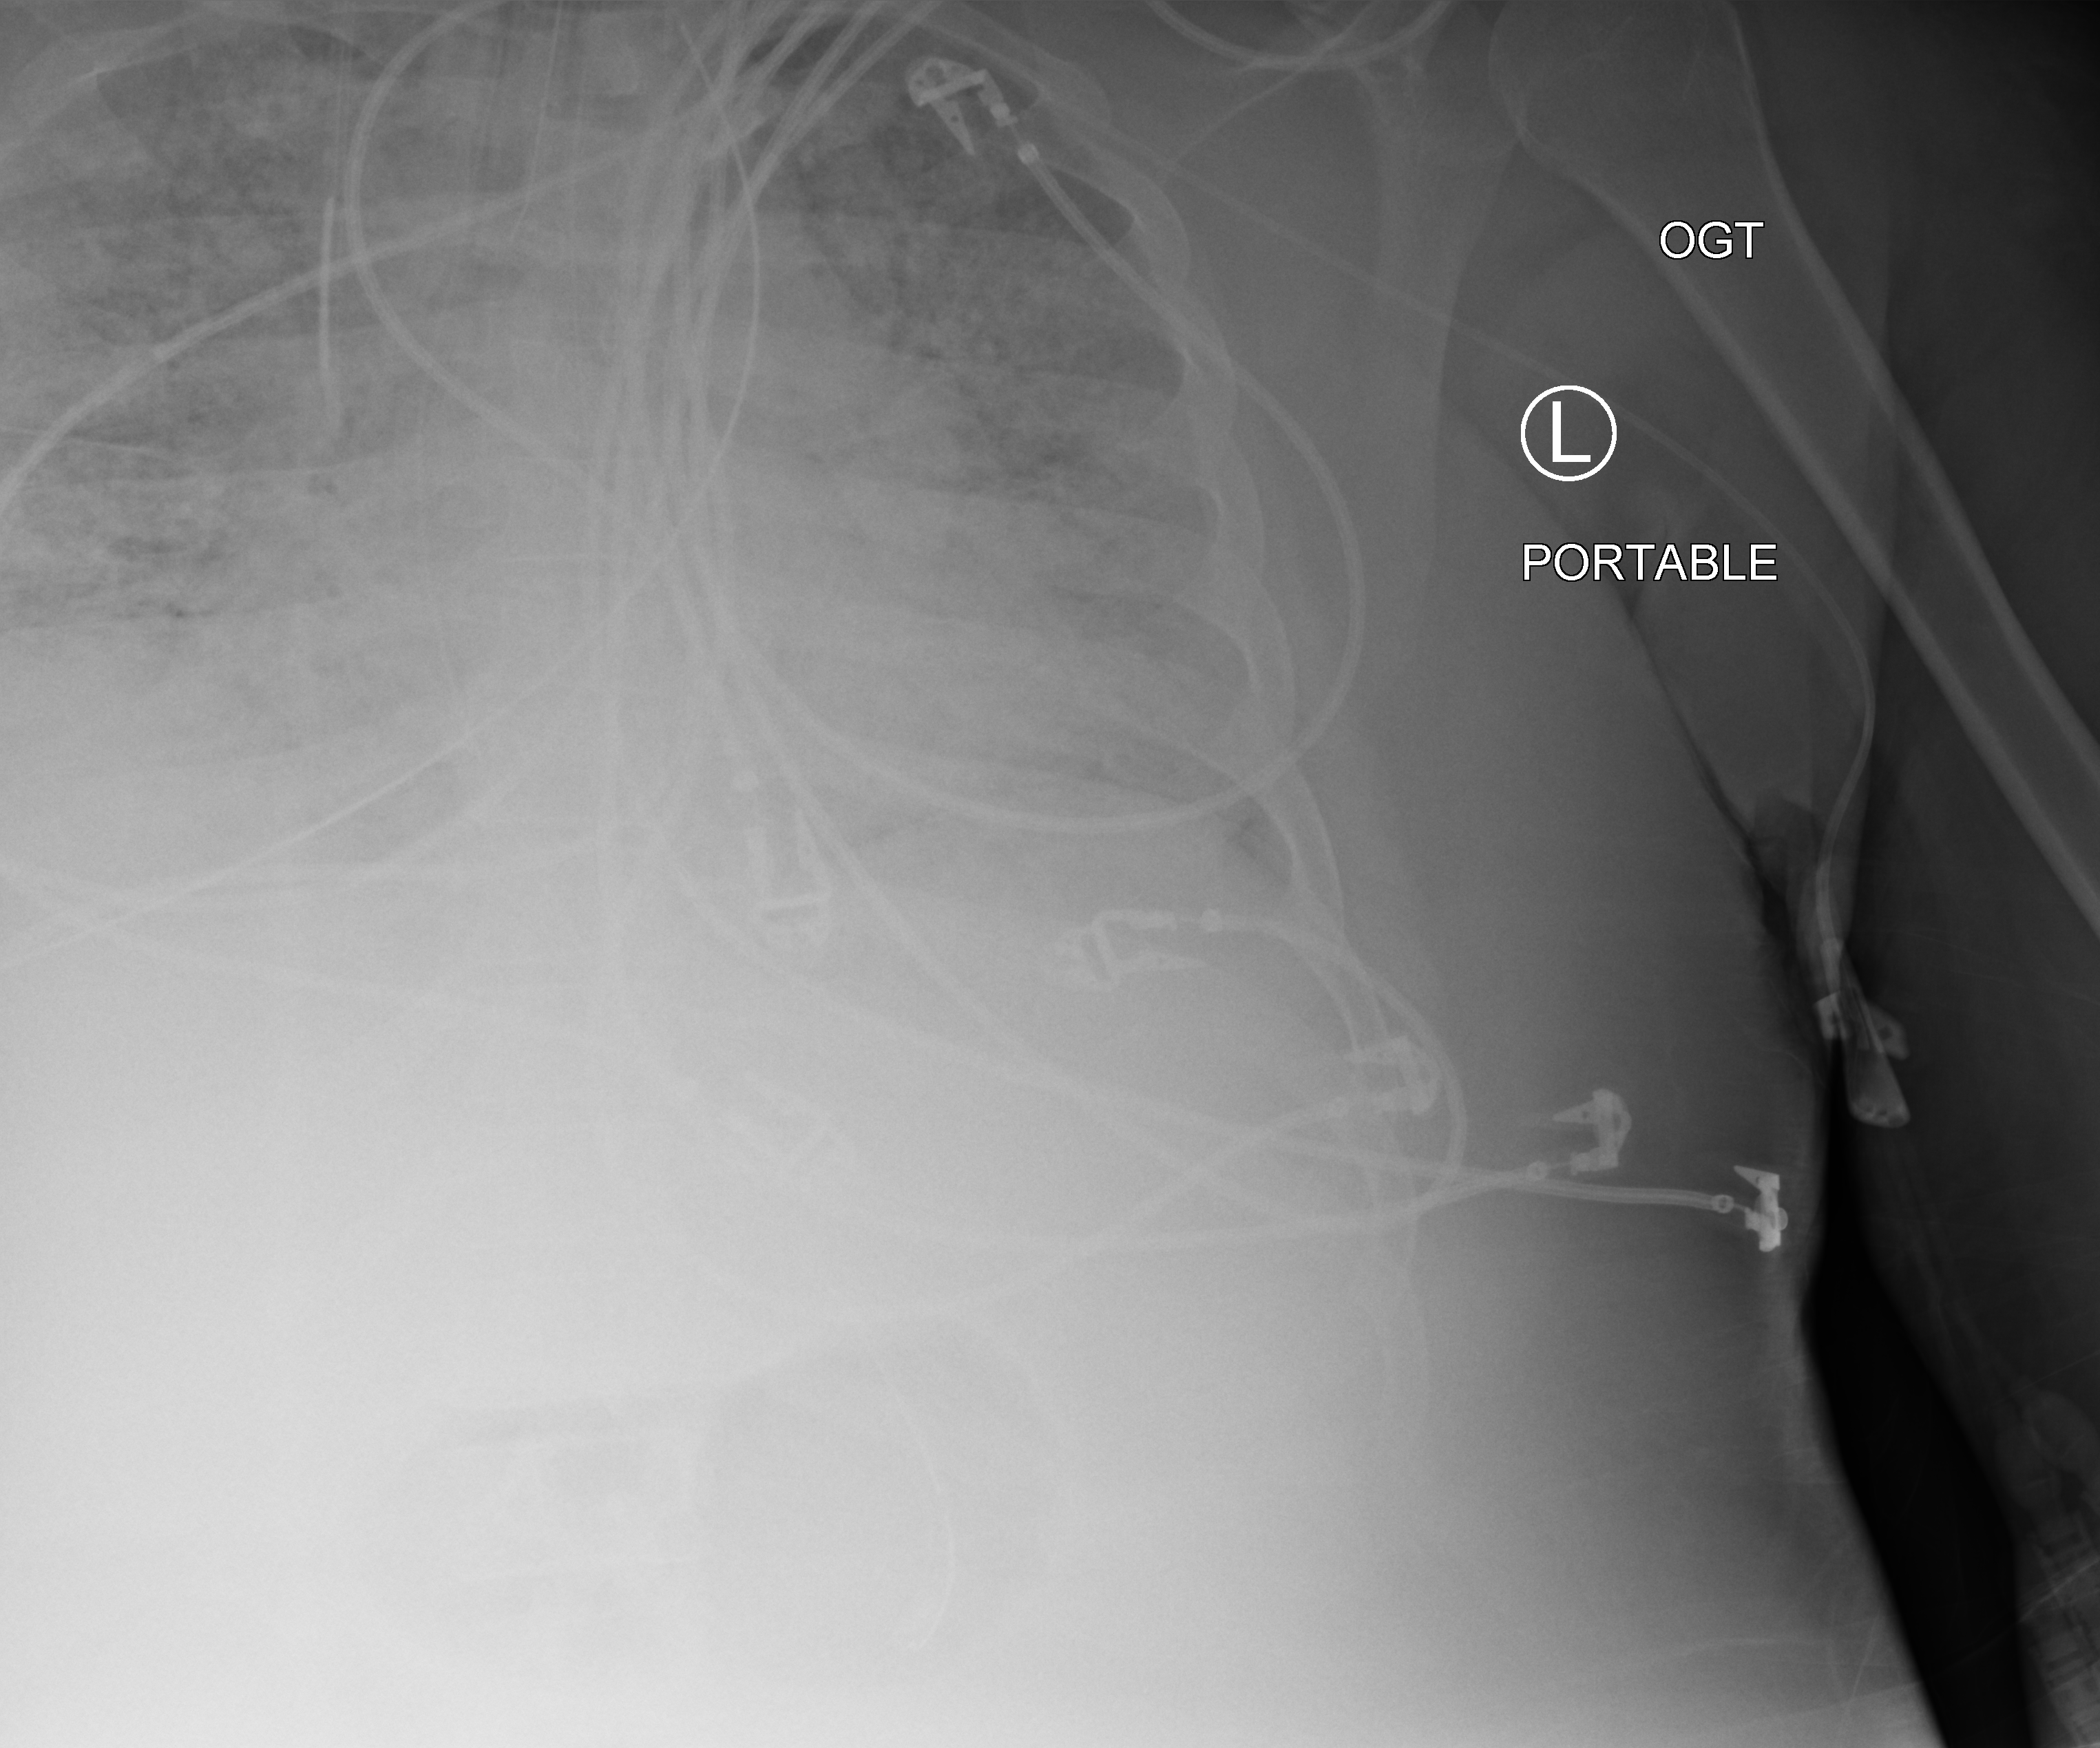
Bedside chest radiograph (computed radiography). Adult patient hospitalised with COVID-19, age 18–59 years.
Admission-level facts for this patient (not findings on this image; timing relative to this image not recorded):
- mechanically ventilated during this hospital stay: yes